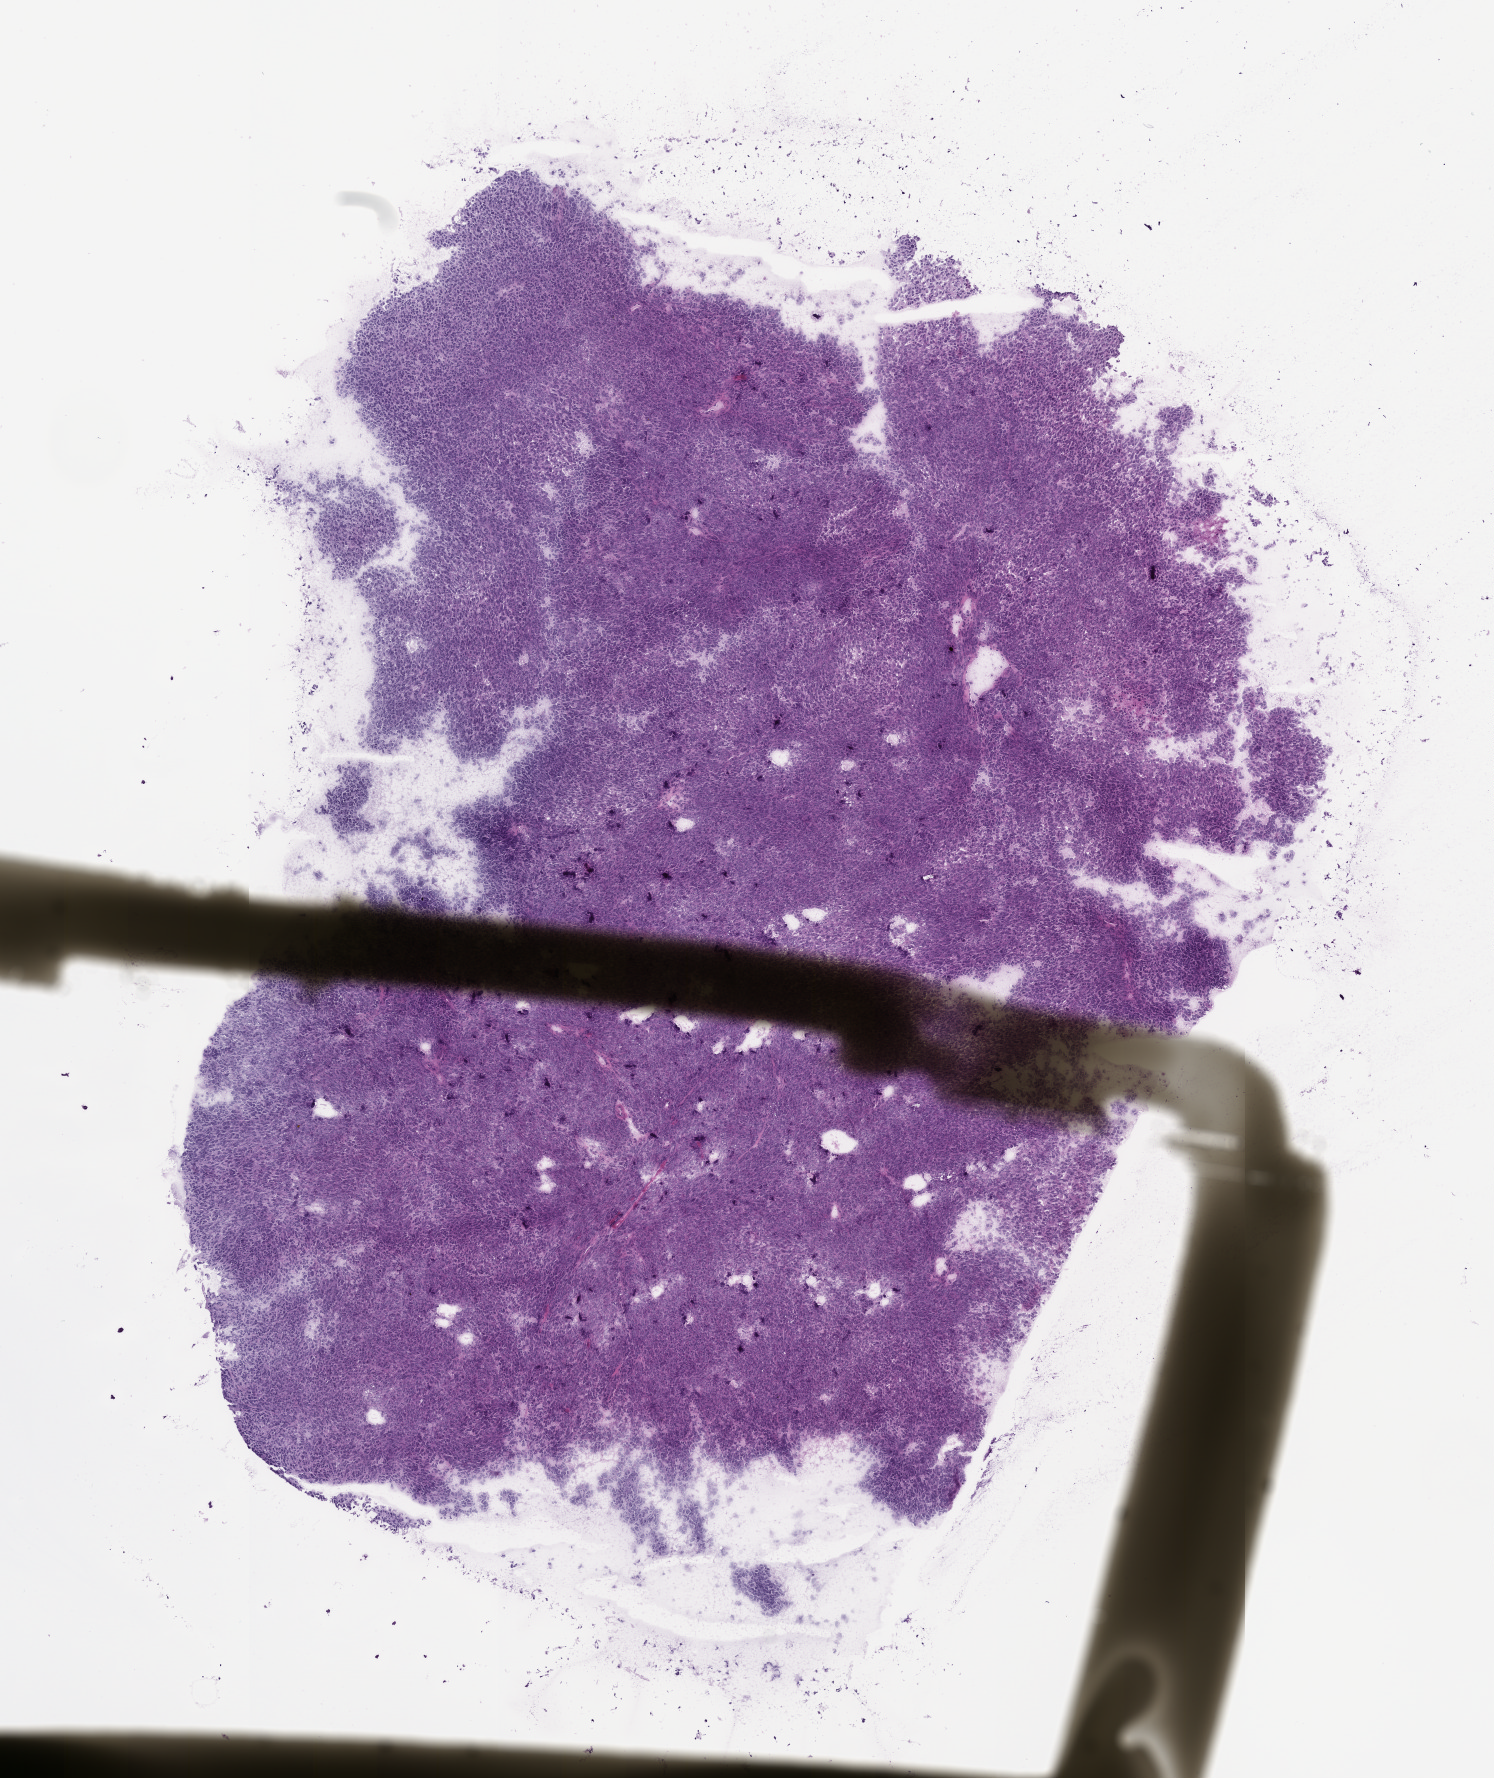
Whole-slide image, hematoxylin and eosin (H&E): patient-derived xenograft (human tumor grown in a mouse) — whole scanned area (about 6.0 x 7.2 mm) shown as a low-resolution overview; formalin-fixed paraffin-embedded section; tumor site category: skin.
Originating patient diagnosis: Melanoma.